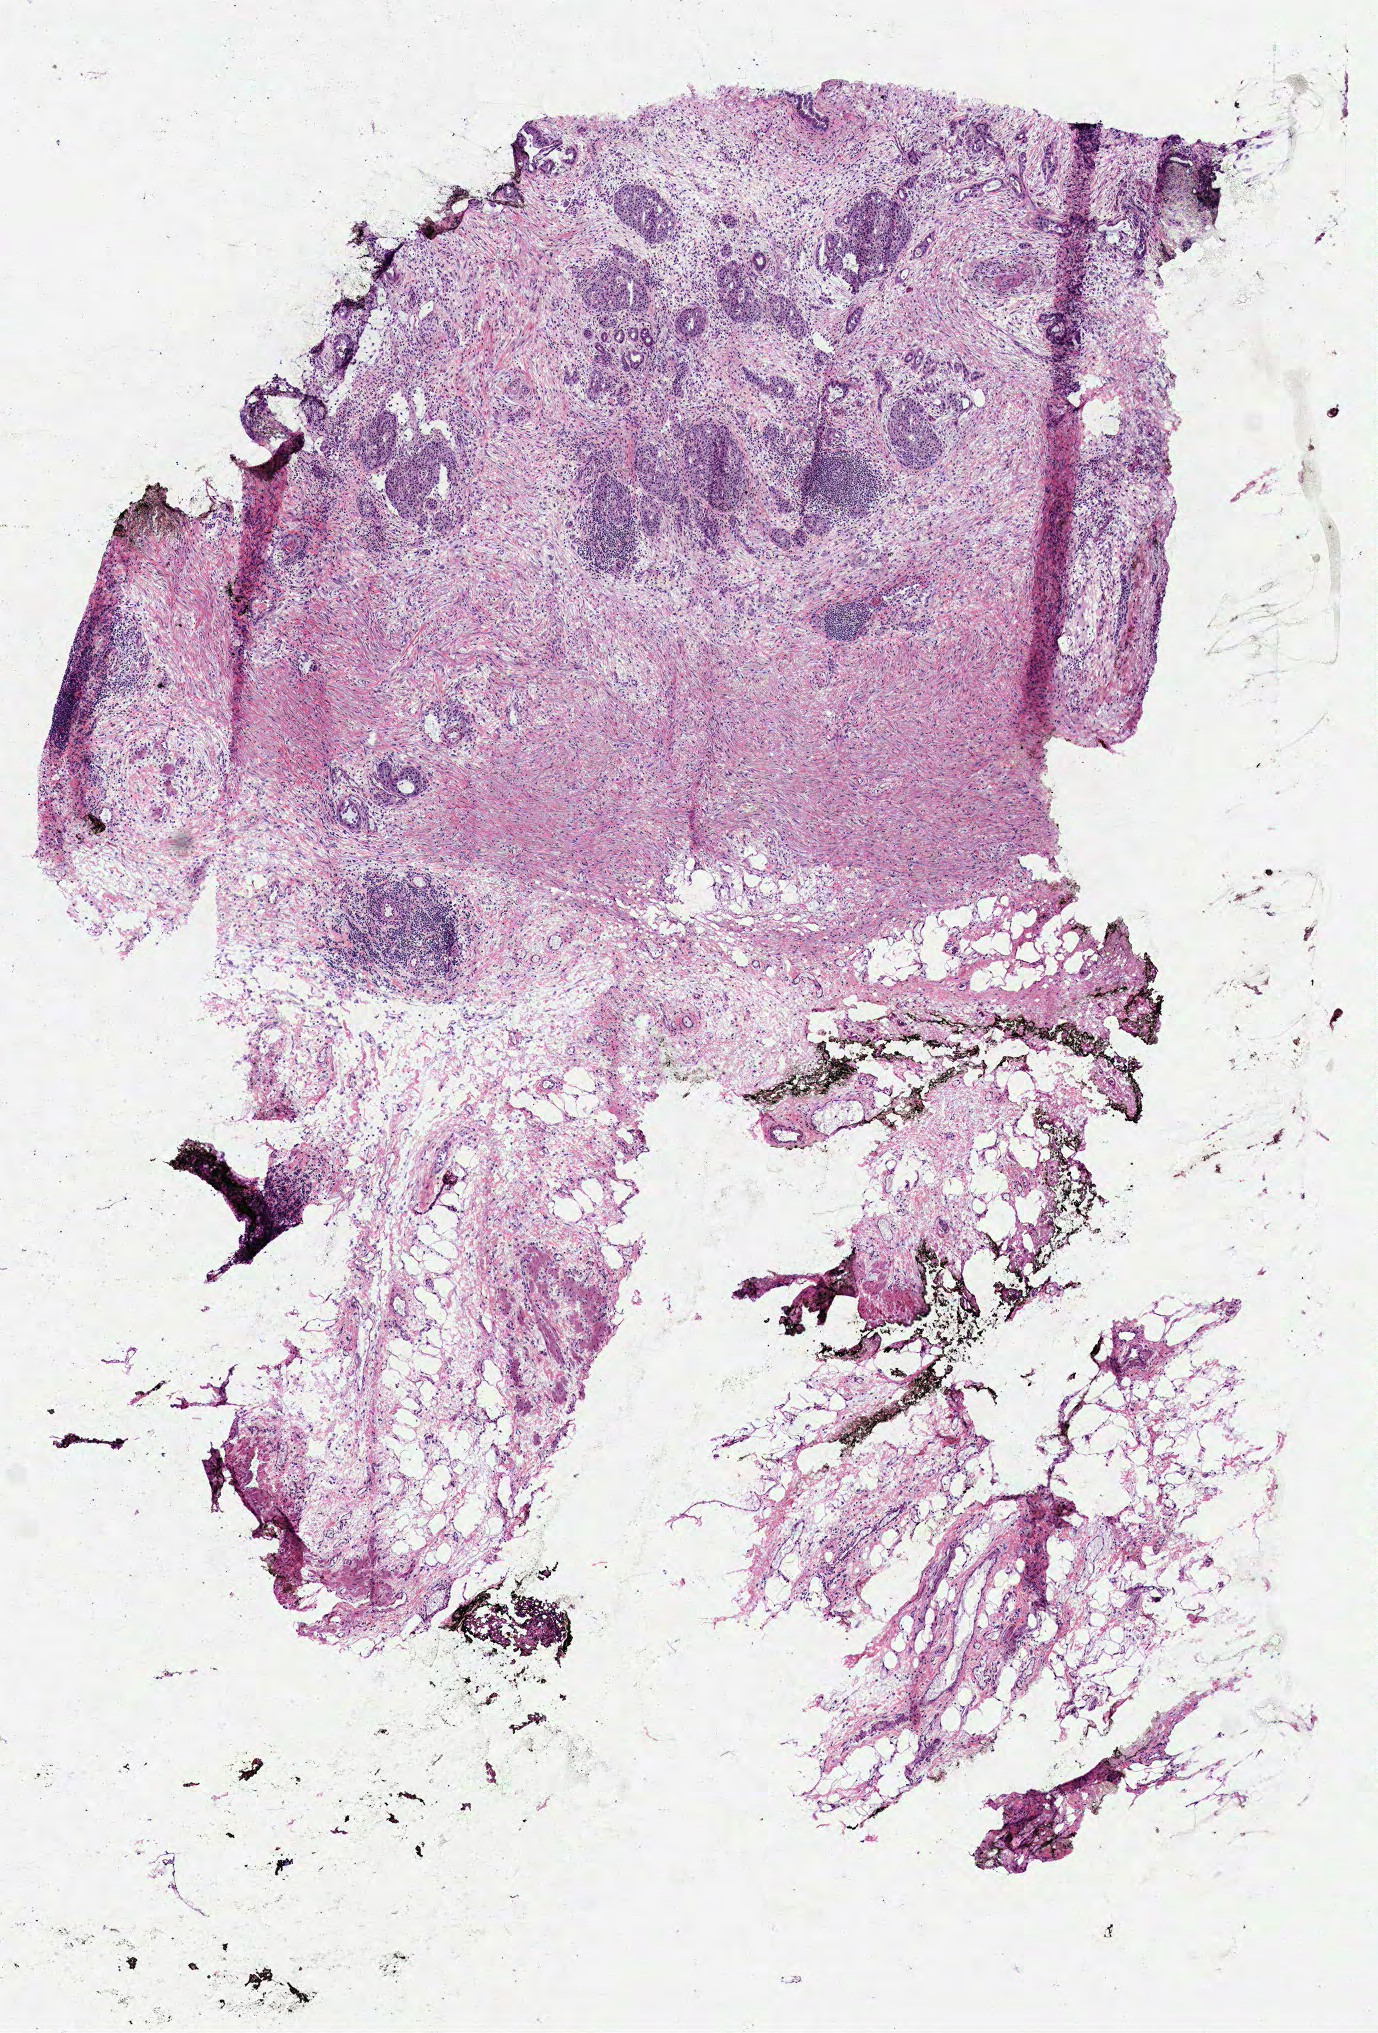
Whole-slide histology image, H&E-stained, shown as a low-resolution overview of the whole scanned area (about 5.6 x 8.2 mm), frozen section, primary tumour sample from the pancreas. Male, age 69 years at initial diagnosis. Histologic grade: G2 (moderately differentiated). Slide review estimates, as recorded: tumour cells 40%, tumour nuclei 40%, normal cells 0%, stromal cells 60%, necrosis 0%.
AJCC pathologic stage: III. Lymph nodes positive (case pathology): 0 of 16 examined. Histologic diagnosis: Infiltrating duct carcinoma, NOS (head of pancreas).